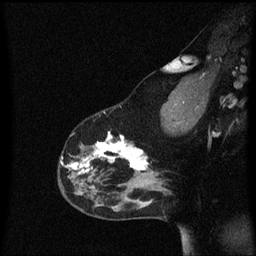
Breast MRI (dynamic contrast-enhanced), one sagittal slice; slice 43 of 60 in the series (ordered by position); dynamic contrast-enhanced series, image 2 of 3 at this slice position (ordered by acquisition); 1.5 T; TE 4.2 ms, TR 8.4 ms; 256 × 256 image matrix, field of view 200 × 200 mm. Patient: female, 33 years.
Annotated regions visible in this slice (semi-automatically segmented with operator editing):
- analysis volume of interest (the breast-tissue region the enhancement analysis was run in; not a lesion): box from (x=59, y=120) to (x=152, y=191) px
- tumour enhancement mask (voxels above the 70 % enhancement threshold inside the analysis volume of interest): (x=61, y=134)–(x=149, y=173)